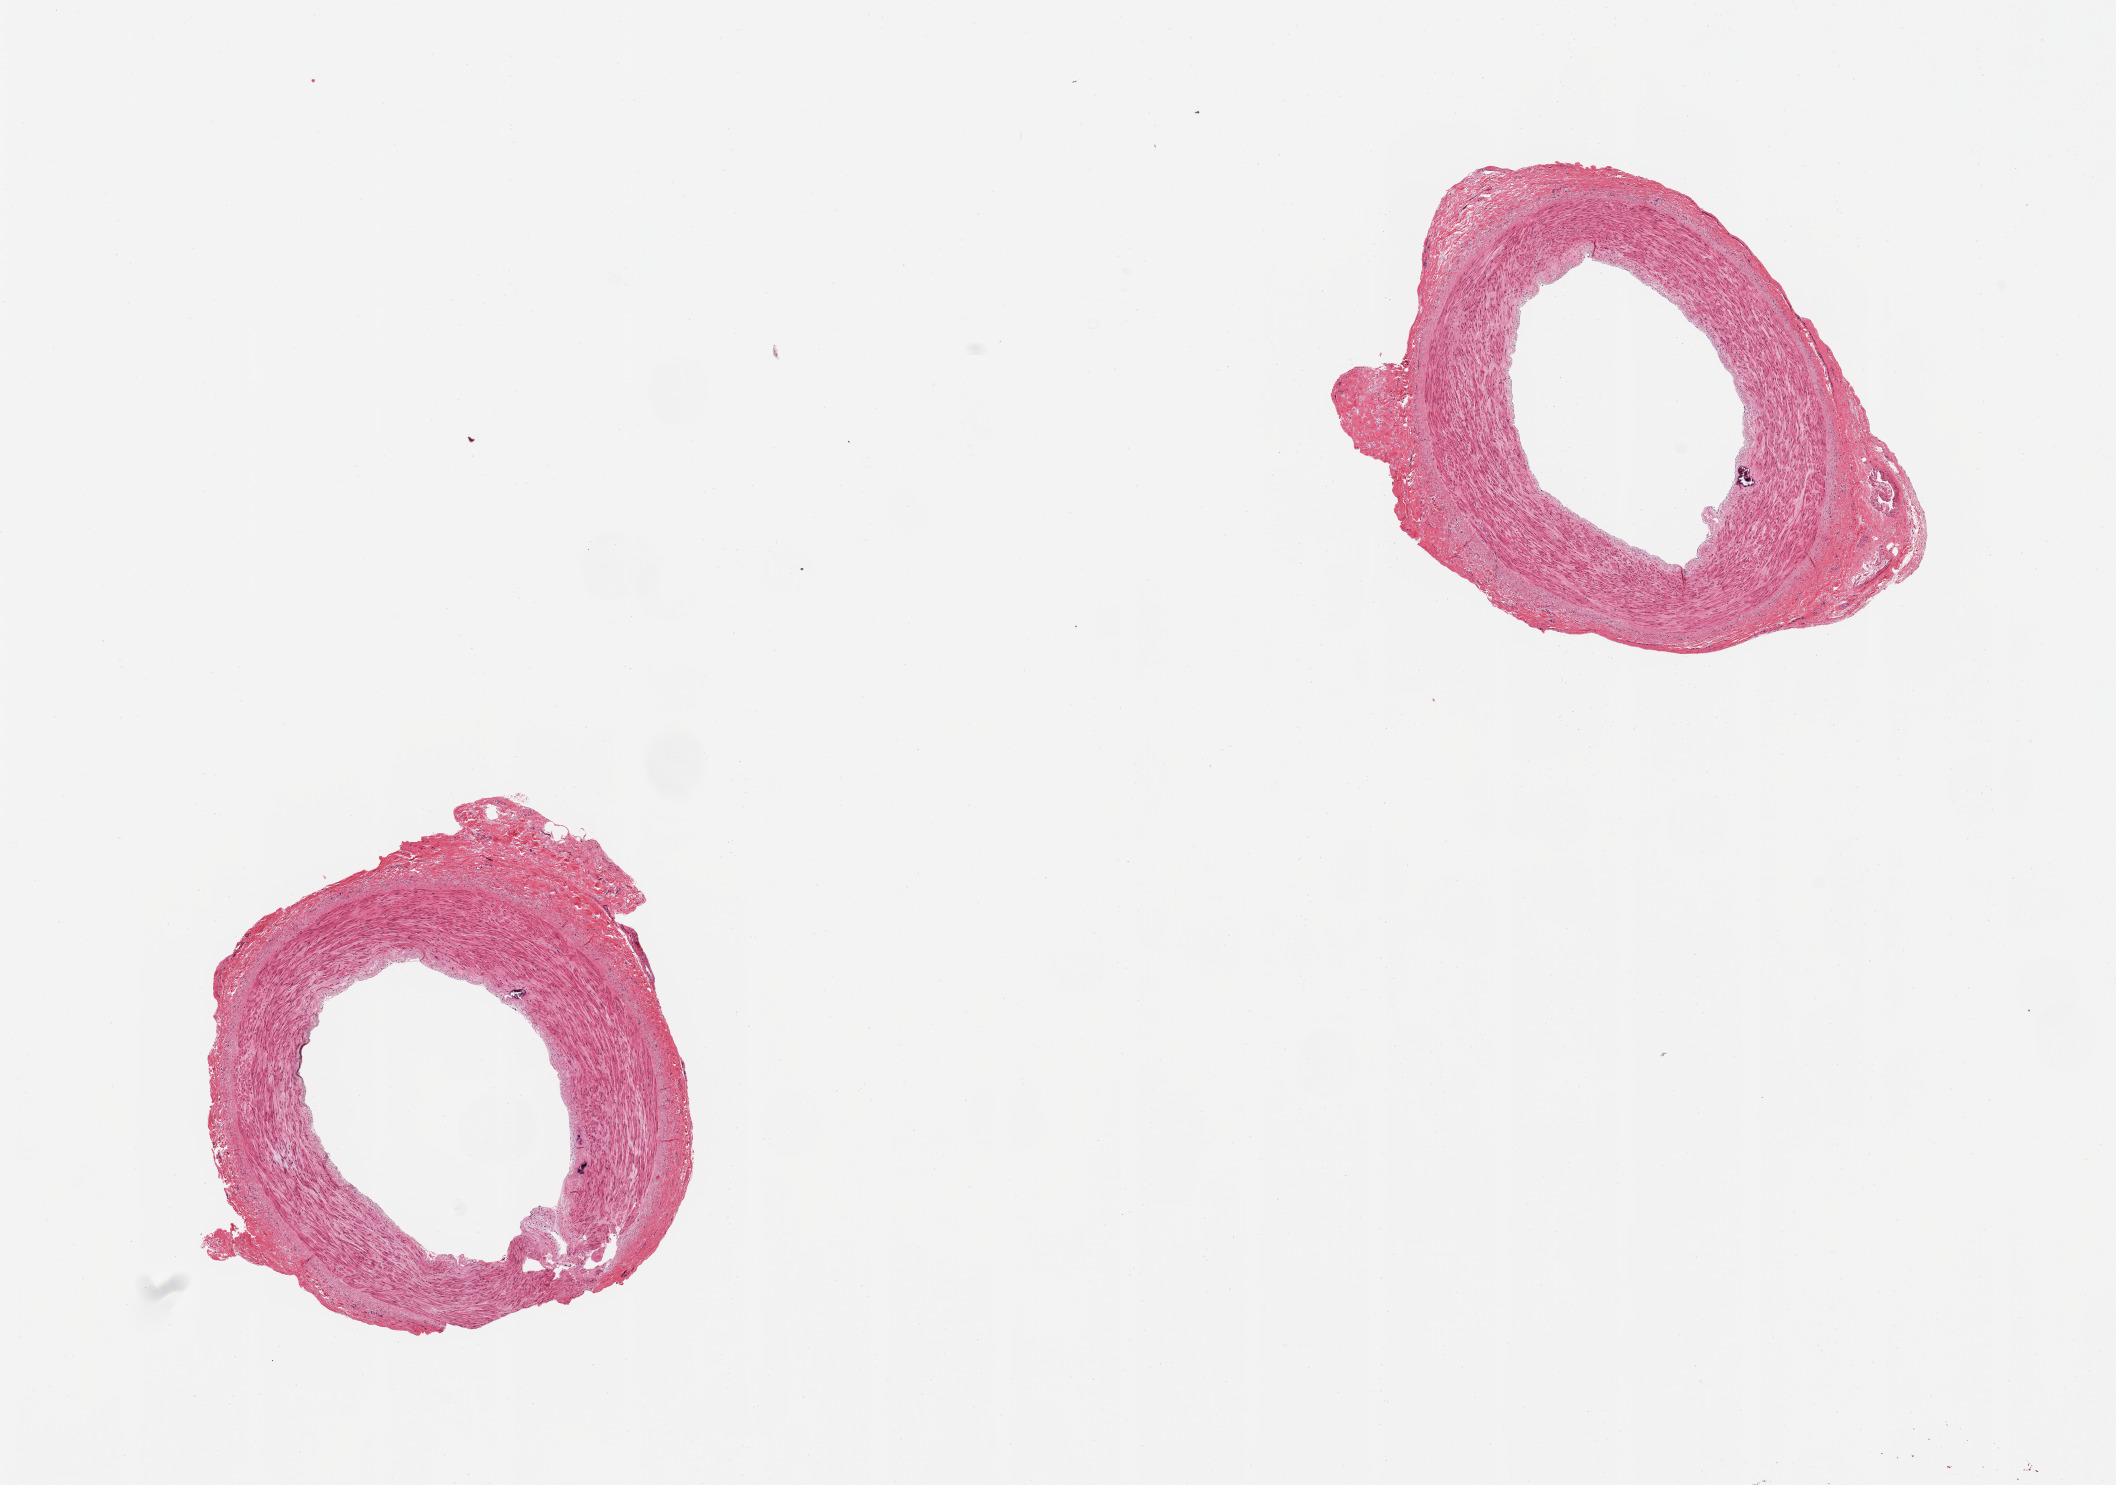
Digitized haematoxylin and eosin-stained section, whole scanned area (about 16.7 x 11.7 mm) shown as a low-resolution overview. PAXgene-fixed, paraffin-embedded tissue. Sampled site (target tissue): tibial artery. Donor tissue sample. Female donor.
Pathologist's review note for this sample: 4 pieces, adherent fat, excellent specimens.